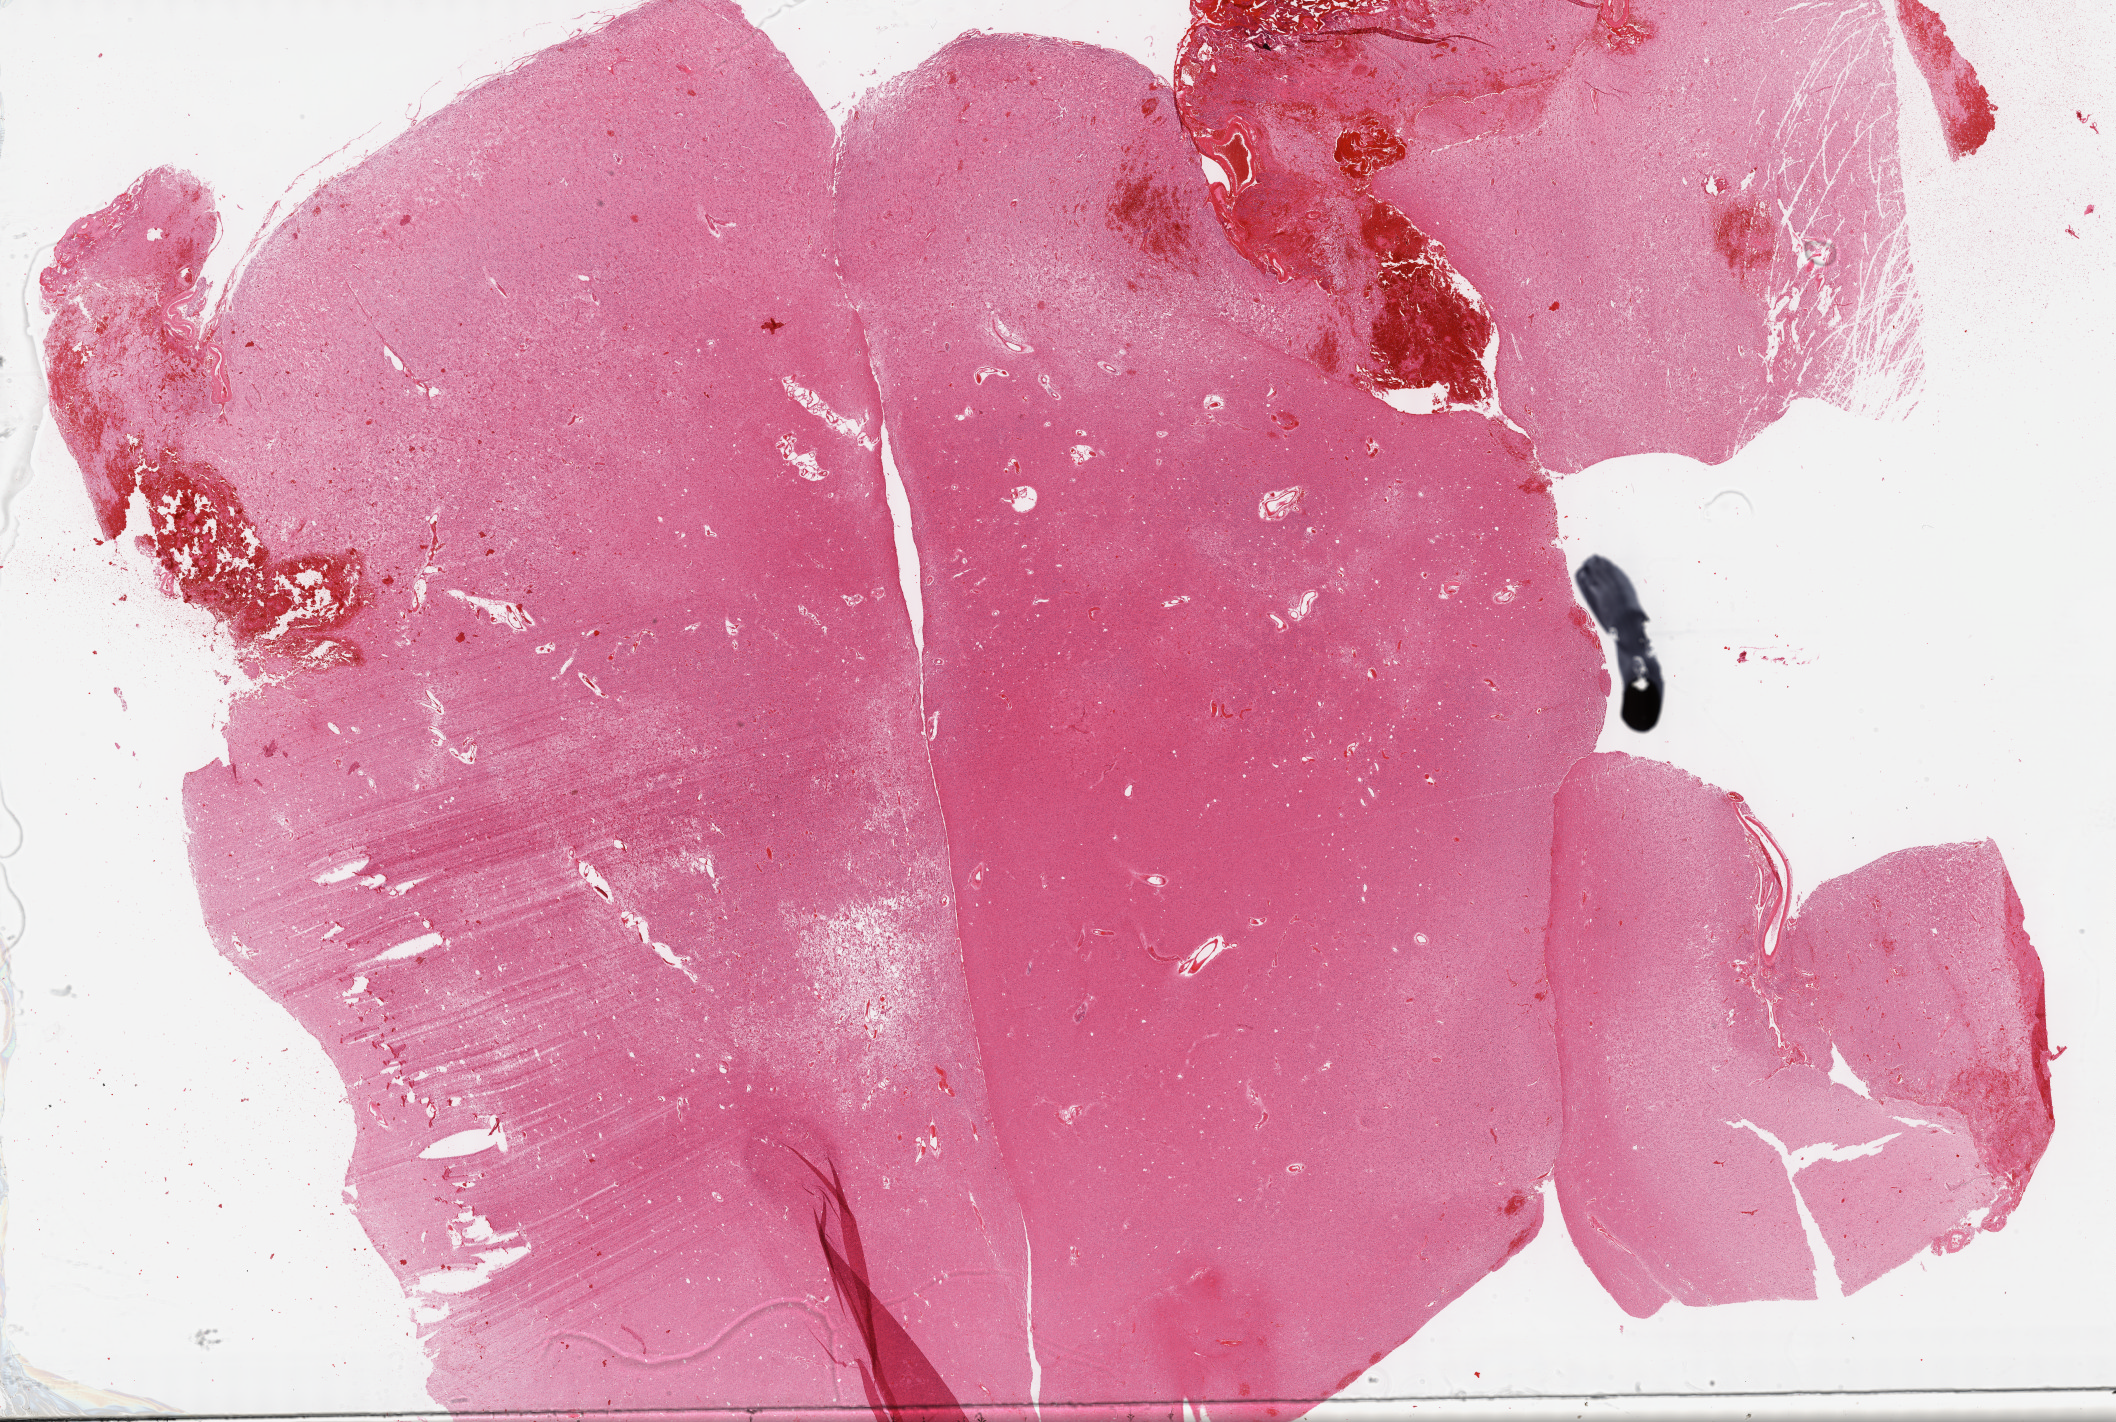
Digitized H&E tissue section (whole slide), a low-resolution overview of the entire scanned area, about 34.2 x 23.0 mm, formalin-fixed paraffin-embedded (FFPE) diagnostic section, sample: primary tumour, brain. Male patient; age at initial diagnosis 46 years. Histologic grade: G3 (poorly differentiated).
• laterality: left
• diagnosis: Oligodendroglioma, anaplastic